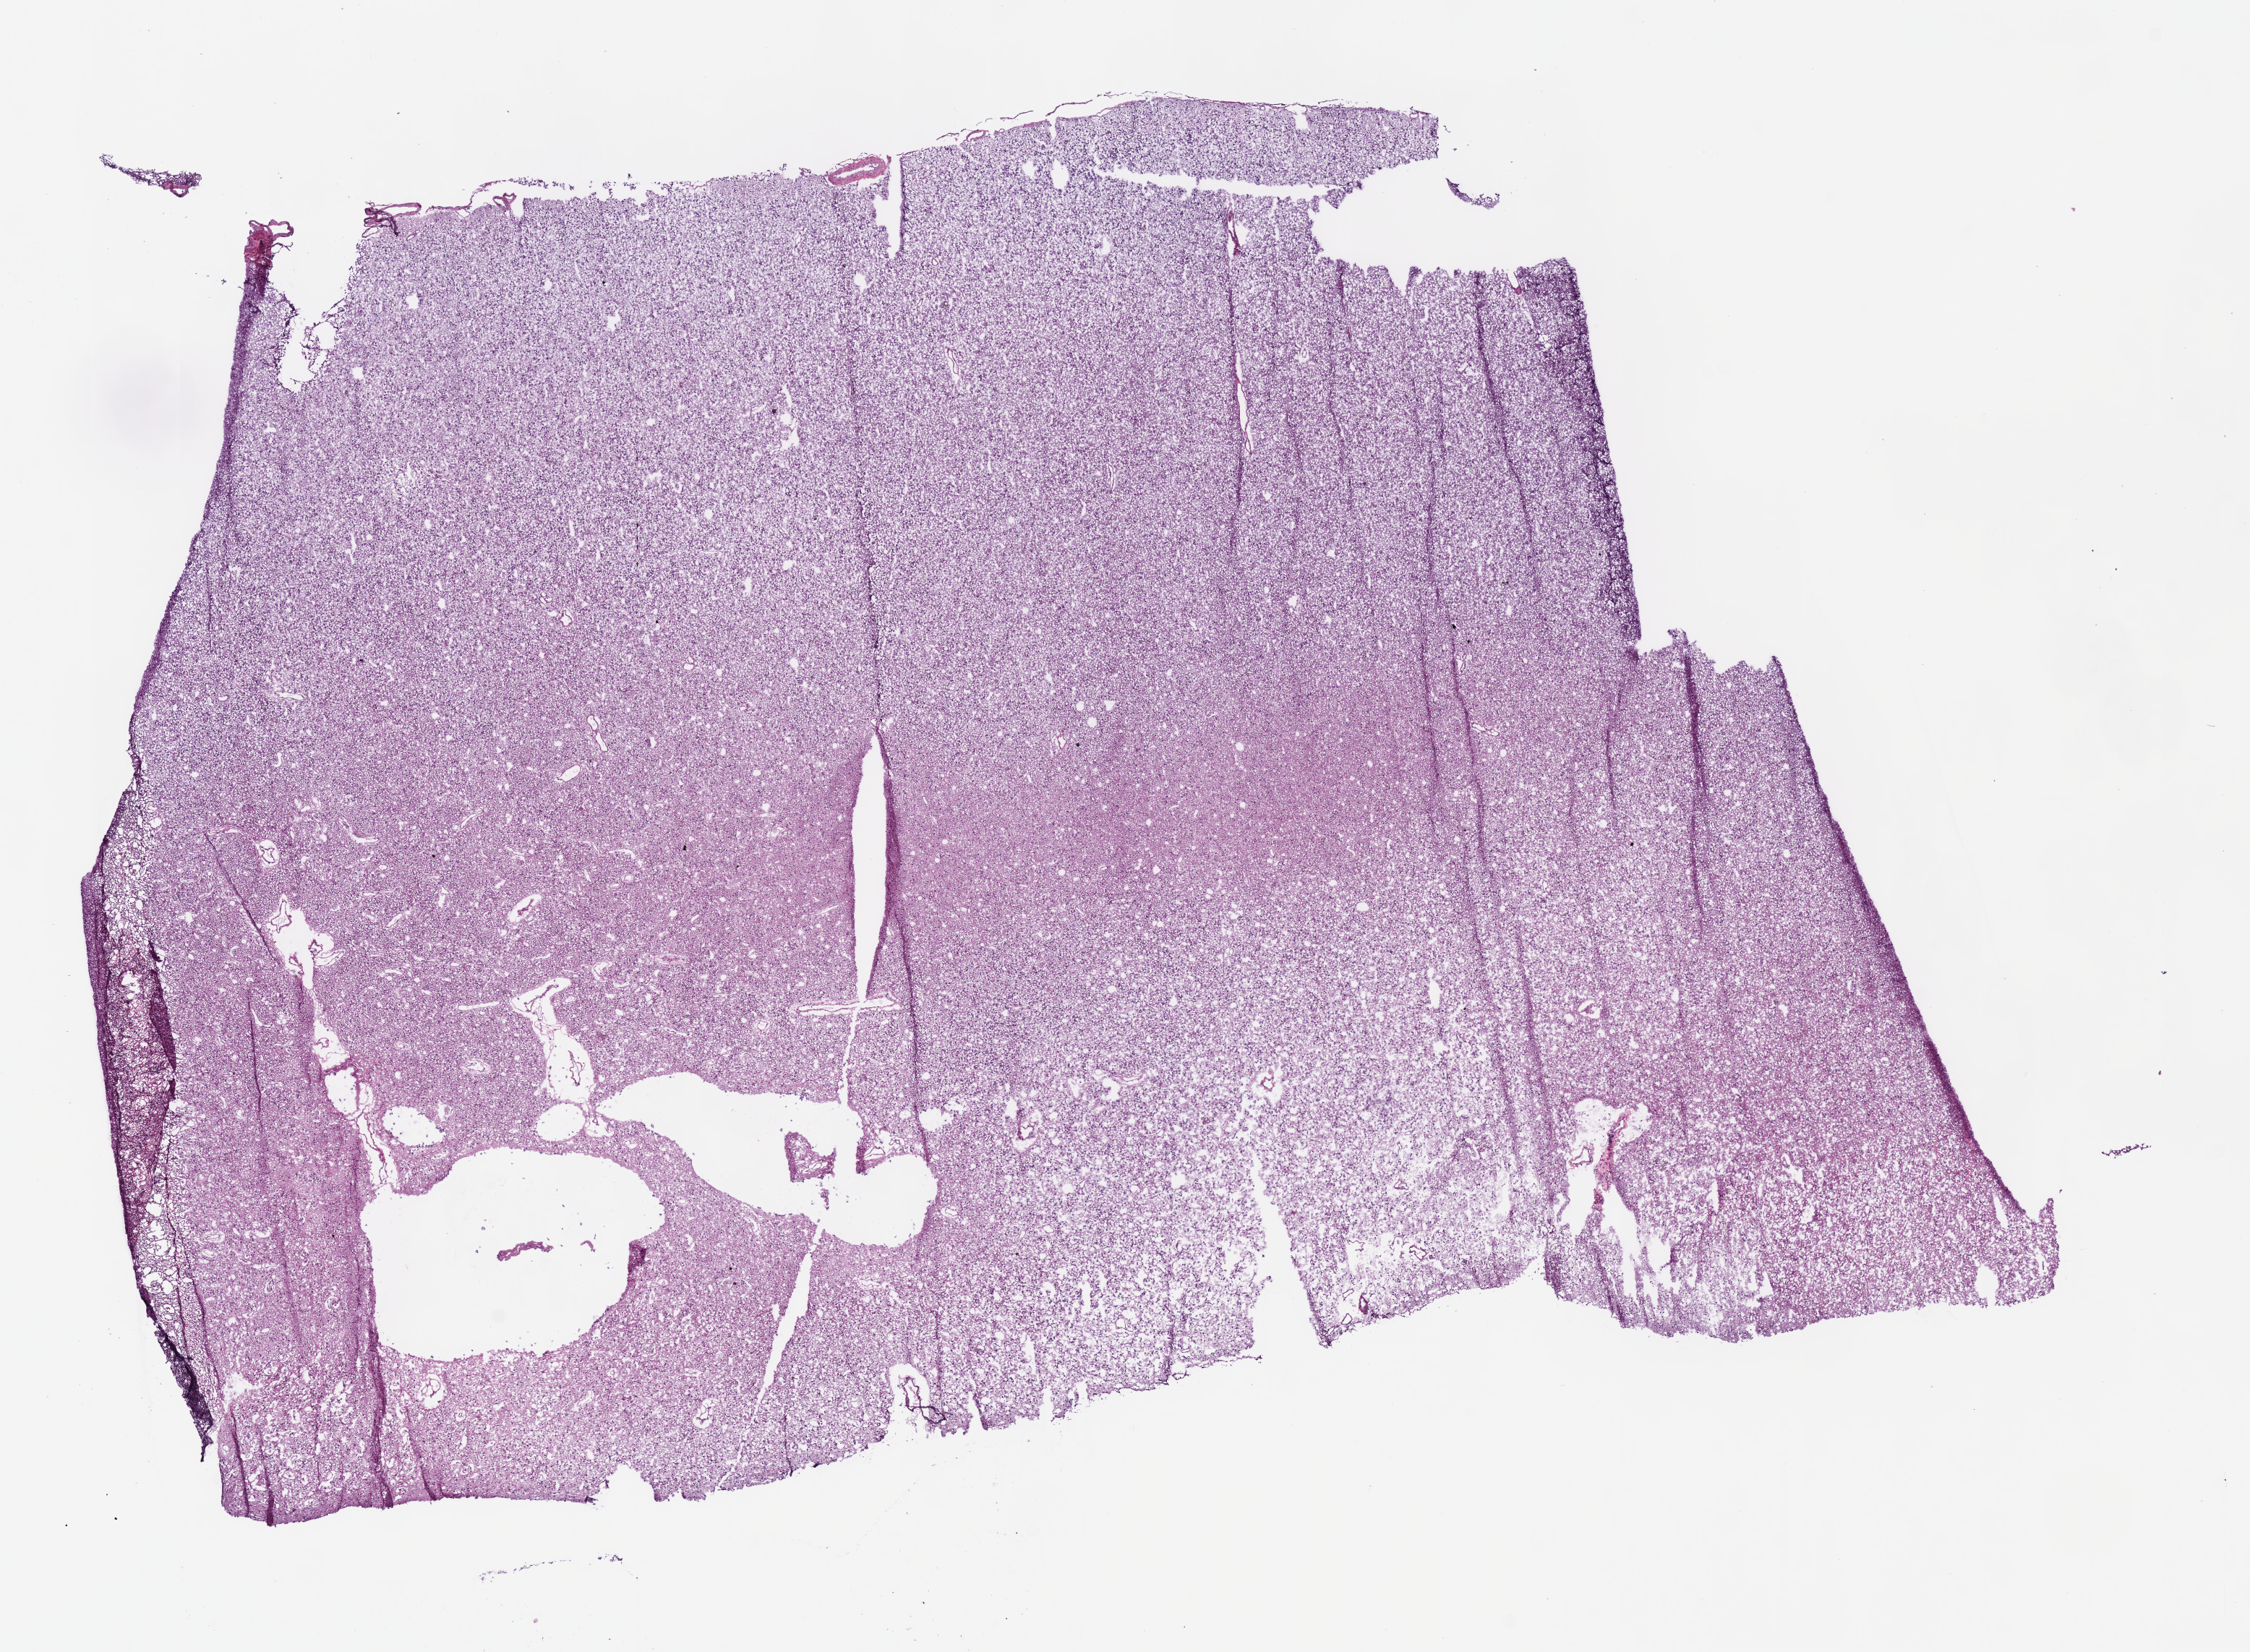
H&E whole-slide image, shown as a low-resolution overview of the whole scanned area (about 12.2 x 9.0 mm, slide scanned at 40x), frozen section, sample: primary tumour, brain. Patient: female, age at initial diagnosis 31 years. Histologic grade: G3 (poorly differentiated). Pathologist review of this section (percent, as recorded): tumour cells 100%, tumour nuclei 65%, normal cells 0%, stromal cells 0%, necrosis 0%.
- pathologic diagnosis: Oligodendroglioma, anaplastic (cerebrum)